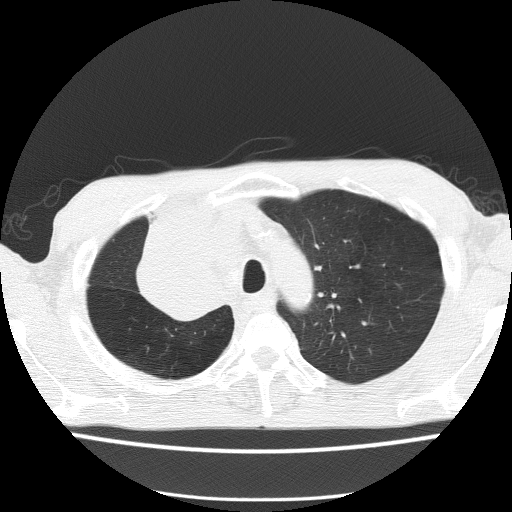
Axial slice from a low-dose chest CT screening exam; baseline annual screen; lung window (W 1500 / L -600 HU); lung (sharp) reconstruction kernel (FC51); 120 kVp; slice 33 of 150 in the series. Male, age 59 years at enrolment.
Expert reader's lesion annotation, bounding box [x1, y1, x2, y2] px = [130, 235, 240, 327]. The screening reader recorded 5 non-calcified nodules or masses ≥4 mm on this exam; which of them this box marks is not recorded. Later outcome: lung cancer diagnosed 72 days after this screen — squamous cell carcinoma, NOS, right upper lobe, moderately differentiated (G2), stage IV (AJCC 6th edition).